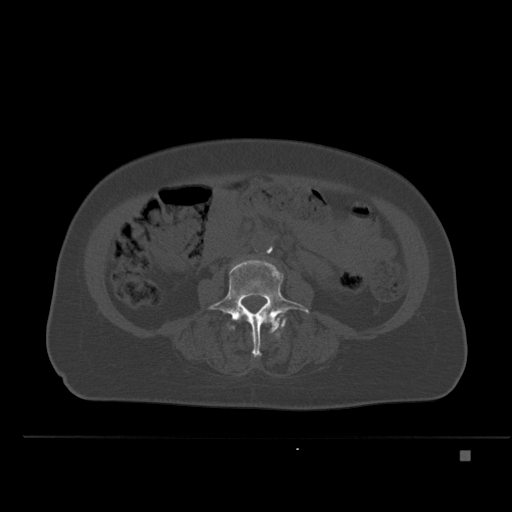
CT including the spine, one axial slice. Position 181 of 477 along the scan axis. Bone window (W 1800 / L 400 HU). 1.5 mm slice thickness. 512 × 512 image matrix, field of view 422 × 422 mm. Female patient, age 74 years. From the clinical record (not read from this slice): primary cancer: colon.
Annotated regions visible in this slice (semi-automatic segmentation, software-assisted and operator-edited):
- L3 vertebra: bounding box <266,312,271,317> (left, top, right, bottom; pixels)
- L4 vertebra: <208,260,309,356>
- L5 vertebra: <275,321,285,331>